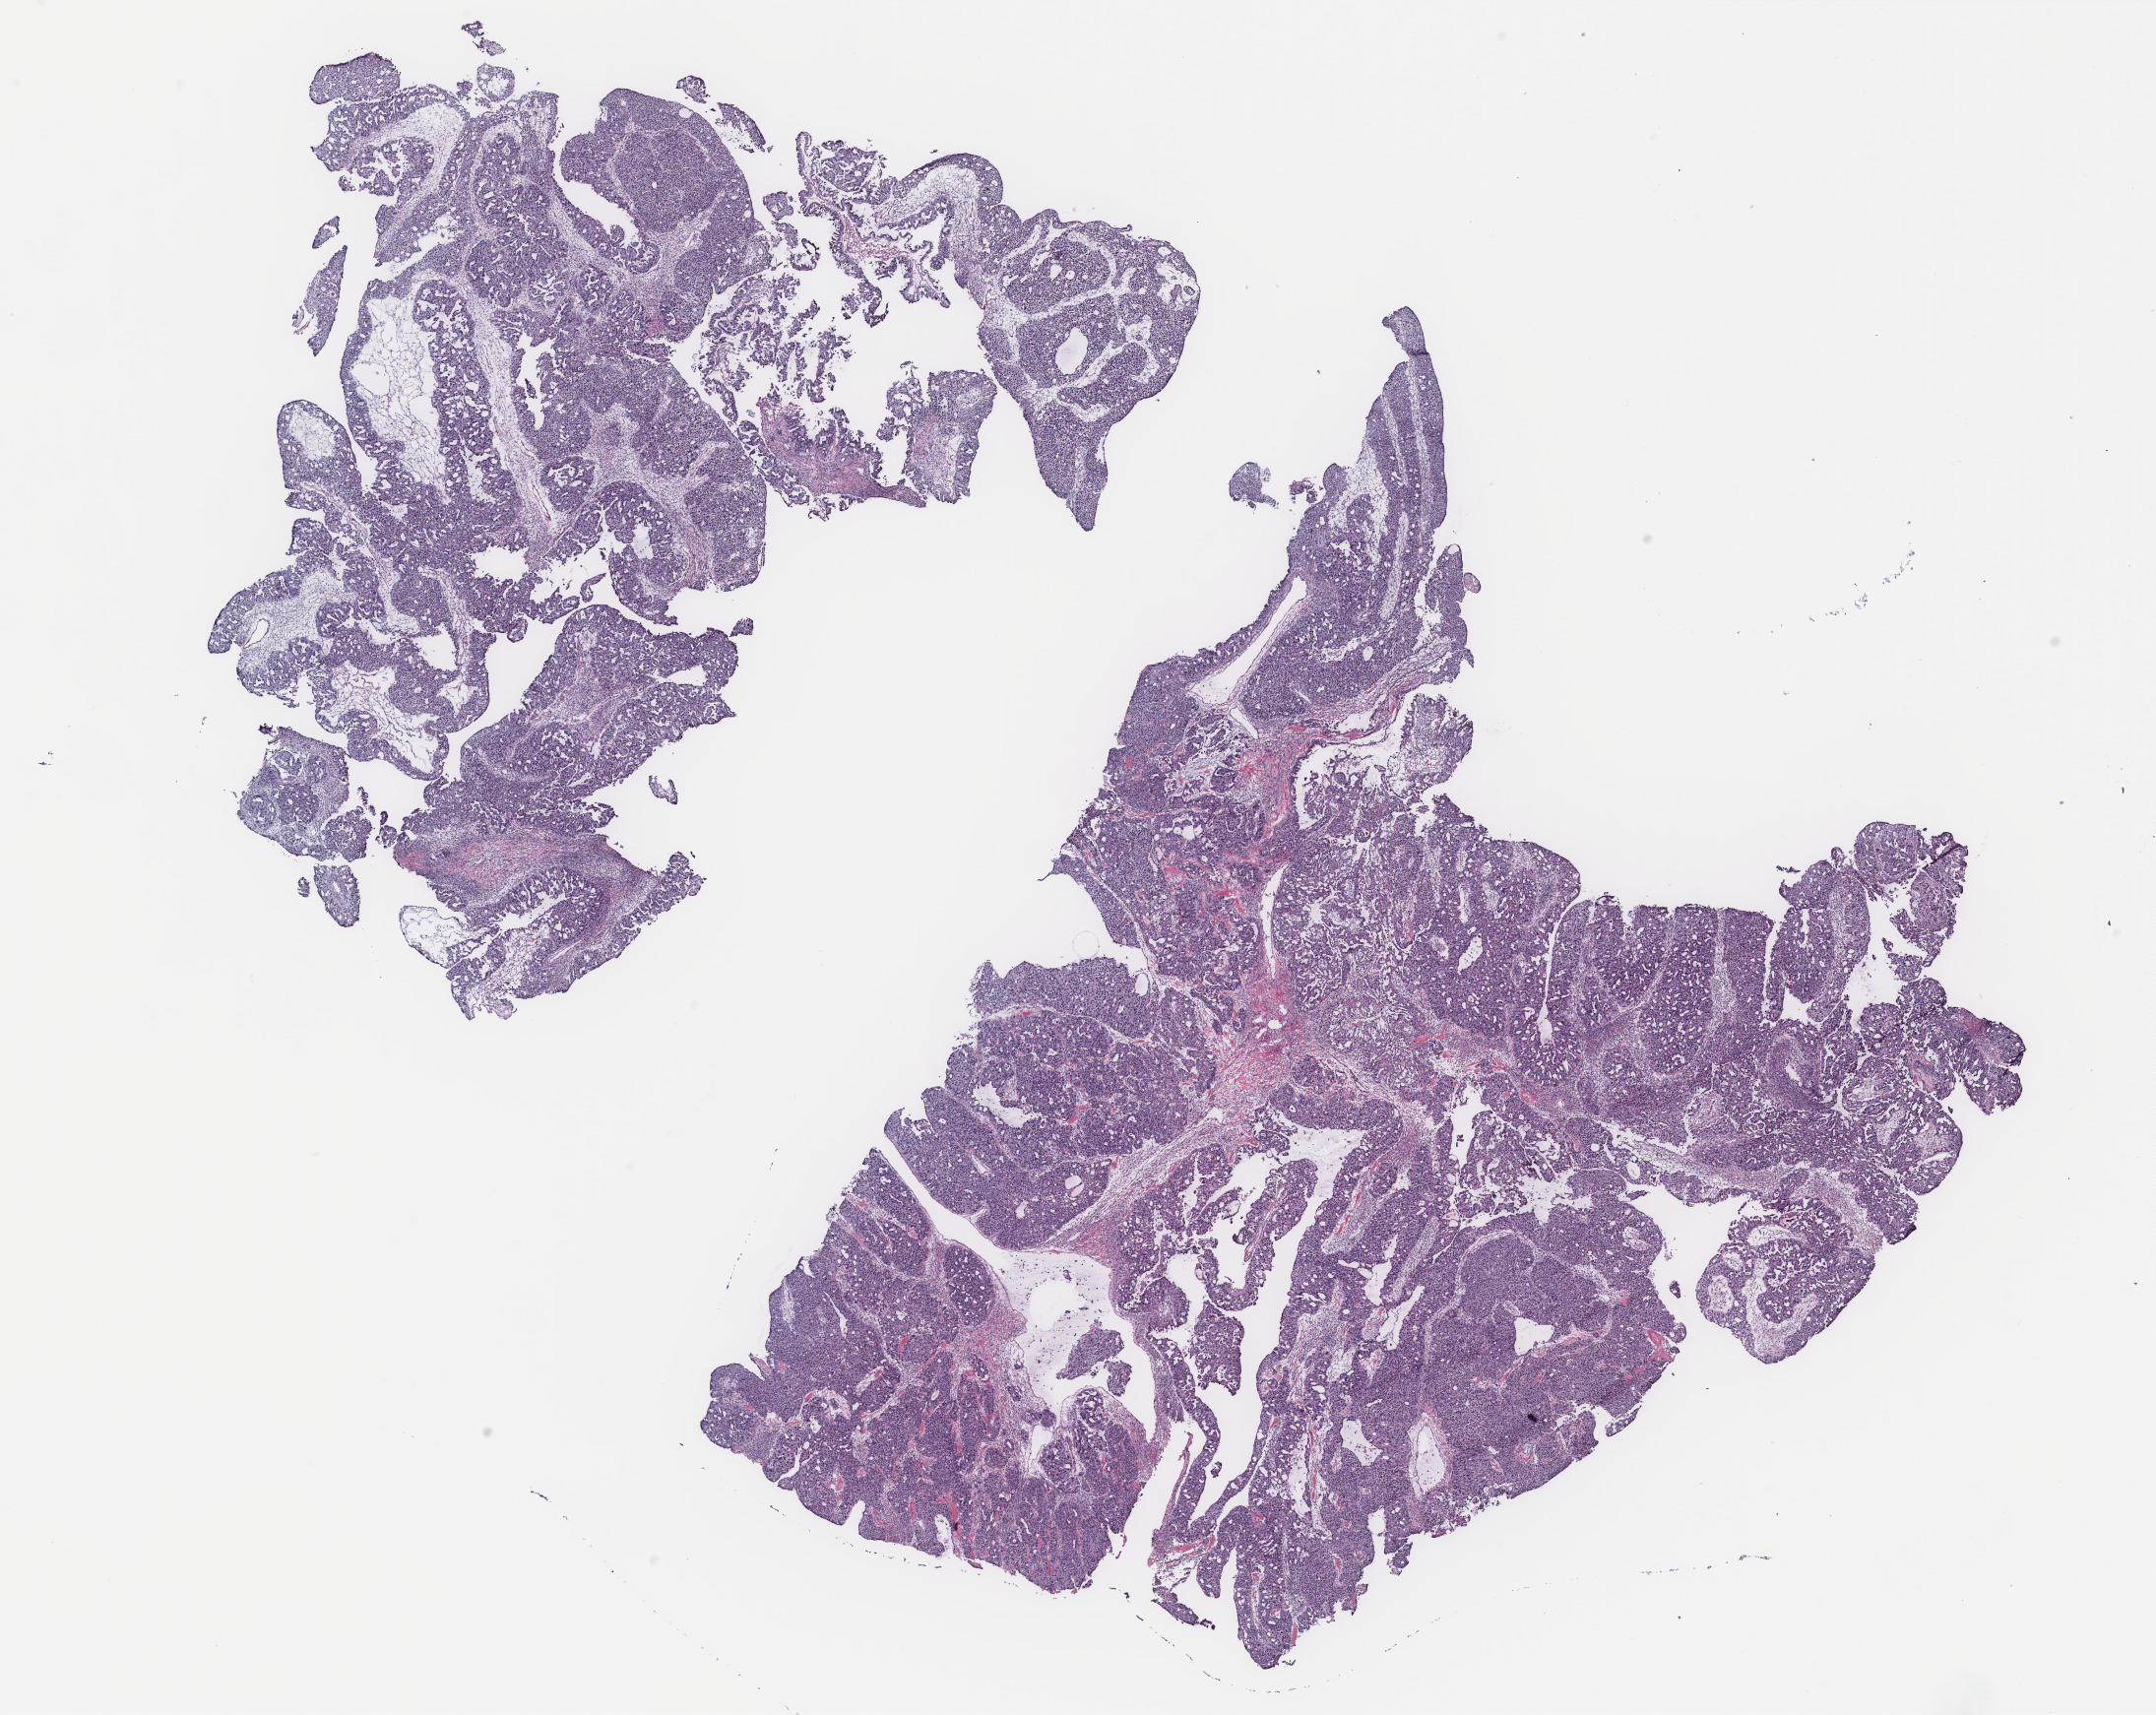
Digitized H&E tissue section (whole slide) — a low-resolution overview of the entire scanned area, about 17.5 x 13.9 mm (acquisition: 40x scan); tumour tissue sample, ovary. 70-year-old female patient.
Primary tumour site (as recorded): ovary. Diagnosis: Serous adenocarcinoma, NOS.